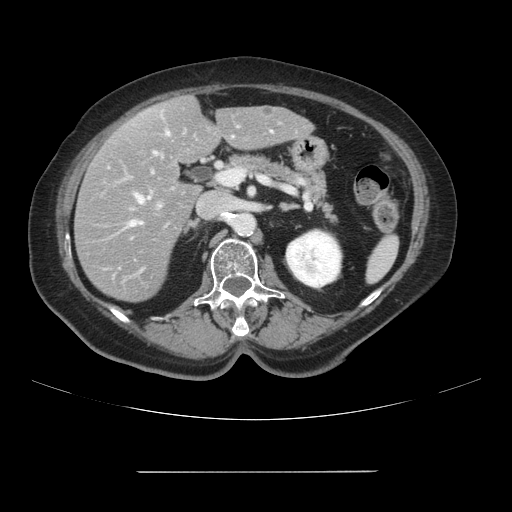
Contrast-enhanced abdominal CT, one axial slice. Position 48 of 111 along the scan axis. 120 kVp. Intravenous contrast given. Soft-tissue window (W 400 / L 40 HU). 512 × 512 image matrix, field of view 400 × 400 mm. Female patient, age 74 years. Case-level facts recorded for this patient, not image findings: diagnosis: colorectal cancer liver metastases, imaged before liver resection; multiple liver metastases: yes.
Structures marked on this image (expert manual segmentation):
- hepatic veins: bounding box (x1, y1, x2, y2) in pixels: (130, 132, 169, 226)
- liver: (75, 96, 312, 302)
- planned liver remnant (the part of the liver to remain after resection): (142, 97, 312, 164)
- portal vein (with intrahepatic branches): (122, 121, 283, 209)
- liver metastasis: (265, 107, 271, 115)